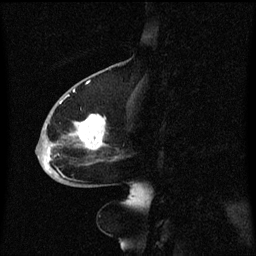
Breast MRI (dynamic contrast-enhanced), one sagittal slice; position 26 of 60 along the scan axis; dynamic contrast-enhanced series, image 2 of 3 at this slice position (ordered by acquisition); 1.5 T; TE 4.2 ms, TR 8.4 ms; 2 mm slice thickness; 256 × 256 image matrix. Patient: female, 68 years. Case-level facts recorded for this patient, not image findings: setting: breast cancer imaged before/during neoadjuvant chemotherapy; receptor status: triple-negative.
Structures marked on this image (semi-automatic segmentation, software-assisted and operator-edited):
- analysis volume of interest (the breast-tissue region the enhancement analysis was run in; not a lesion): bounding box (x1, y1, x2, y2) in pixels: (36, 94, 120, 173)
- tumour enhancement mask (voxels above the 70 % enhancement threshold inside the analysis volume of interest): (44, 102, 107, 173)